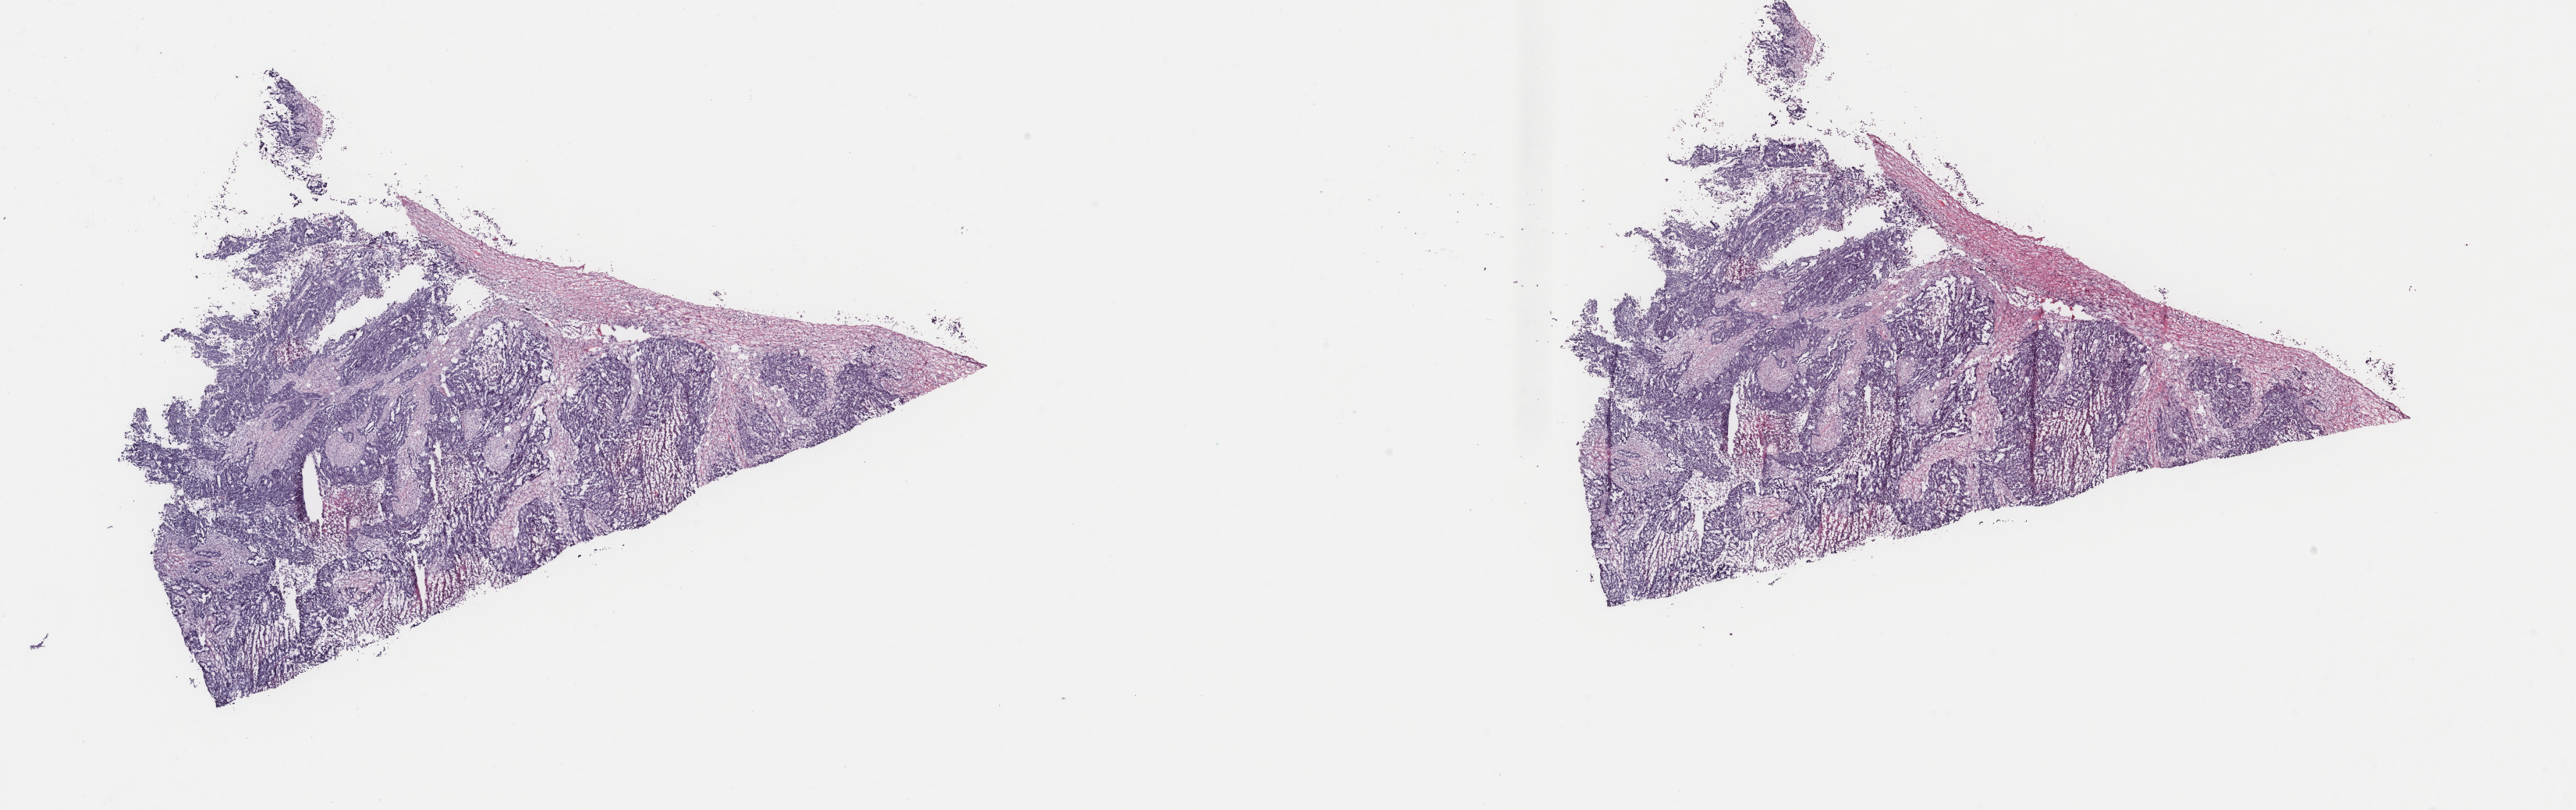
H&E-stained whole-slide image — a low-resolution overview of the entire scanned area, about 26.2 x 8.2 mm (from a 40x scan). Frozen section from the top of the tissue portion. Primary tumour sample from the ovary. Female, age 66 years at initial diagnosis. Histologic grade: G3 (poorly differentiated). Slide review estimates, as recorded: tumour cells 80%, tumour nuclei 80%, normal cells 0%, stromal cells 10%, necrosis 10%. Inflammatory infiltration, as recorded: lymphocyte infiltration 0%, monocyte infiltration 0%, neutrophil infiltration 5%.
- histologic diagnosis: Papillary serous cystadenocarcinoma (specified parts of peritoneum)
- FIGO stage: IIIC